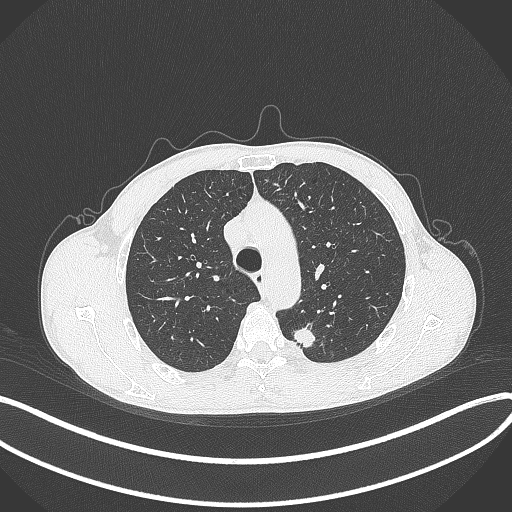
Chest CT, one axial slice. Position 293 of 429 along the scan axis. Reconstruction kernel B70f. Lung window (W 1500 / L -600 HU). 512 × 512 image matrix. Patient: male, 51 years. Case-level facts recorded for this patient, not image findings: clinical TNM (as recorded): T2a N1 M1.
Annotated regions visible in this slice (rectangle marked by the reading radiologist):
- lung tumour (recorded histology: adenocarcinoma): bounding box [x1, y1, x2, y2] px = [288, 323, 323, 352]